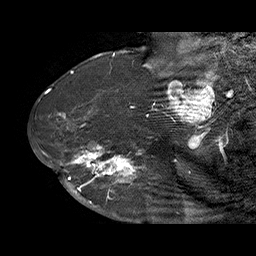
Breast MRI (dynamic contrast-enhanced), one sagittal slice. Dynamic contrast-enhanced series, time point 2 of 6 at this slice position (early post-contrast). 1.5 T. TE 4.5 ms, TR 32.4 ms. 256 × 256 image matrix, field of view 180 × 180 mm. Female patient. From the clinical record (not read from this slice): setting: breast cancer imaged before/during neoadjuvant chemotherapy; receptor status: HR-positive, HER2-negative.
Outlined on this slice (semi-automatic segmentation, software-assisted and operator-edited):
- analysis volume of interest (the breast-tissue region the enhancement analysis was run in; not a lesion): bounding box [x1, y1, x2, y2] px = [71, 128, 159, 202]
- tumour enhancement mask (voxels above the 100 % enhancement threshold inside the analysis volume of interest): [71, 144, 145, 202]